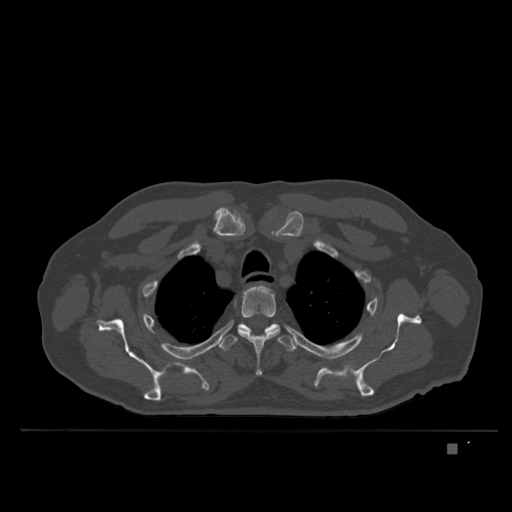
CT including the spine, one axial slice. Slice 297 of 435 in the series (ordered by position). Bone window (W 1800 / L 400 HU). 1.5 mm slice thickness. 512 × 512 image matrix, field of view 434 × 434 mm. Male patient, age 73 years. Case-level facts recorded for this patient, not image findings: primary cancer: skin.
Structures marked on this image (semi-automatic segmentation, software-assisted and operator-edited):
- T3 vertebra: bounding box [x1, y1, x2, y2] px = [237, 285, 280, 376]
- T4 vertebra: [219, 323, 297, 352]